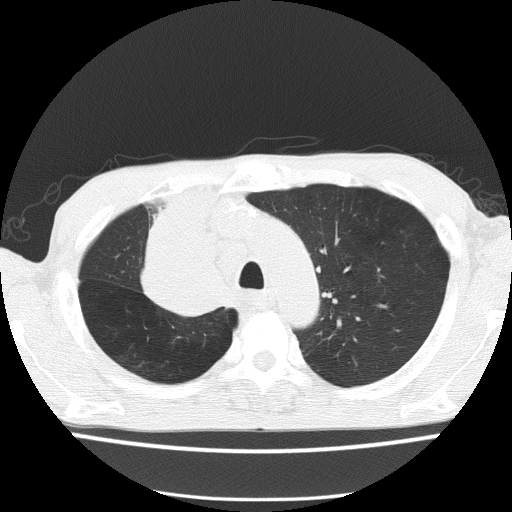
Low-dose screening chest CT, axial slice, baseline screening round, lung window (W 1500 / L -600 HU), 2 mm slice thickness, lung (sharp) reconstruction kernel (FC51), 512 × 512 image matrix, field of view 336 × 336 mm. Male participant, aged 59 years at enrolment. Former smoker at enrolment.
• Lesion marked by an expert reader, bounding box (x1, y1, x2, y2) in pixels: (132, 234, 239, 326).
• The screening reader recorded 5 non-calcified nodules or masses ≥4 mm on this exam (left upper lobe, left upper lobe, left upper lobe, right middle lobe, right lower lobe); which of them this box marks is not recorded.
• Official screen result: positive, change unspecified: nodule(s) >= 4 mm or enlarging nodule(s), mass(es), or other non-specific abnormalities suspicious for lung cancer.
• Participant outcome: lung cancer diagnosed 72 days after this screen — squamous cell carcinoma, NOS, right upper lobe, moderately differentiated (G2), stage IV (AJCC 6th edition).